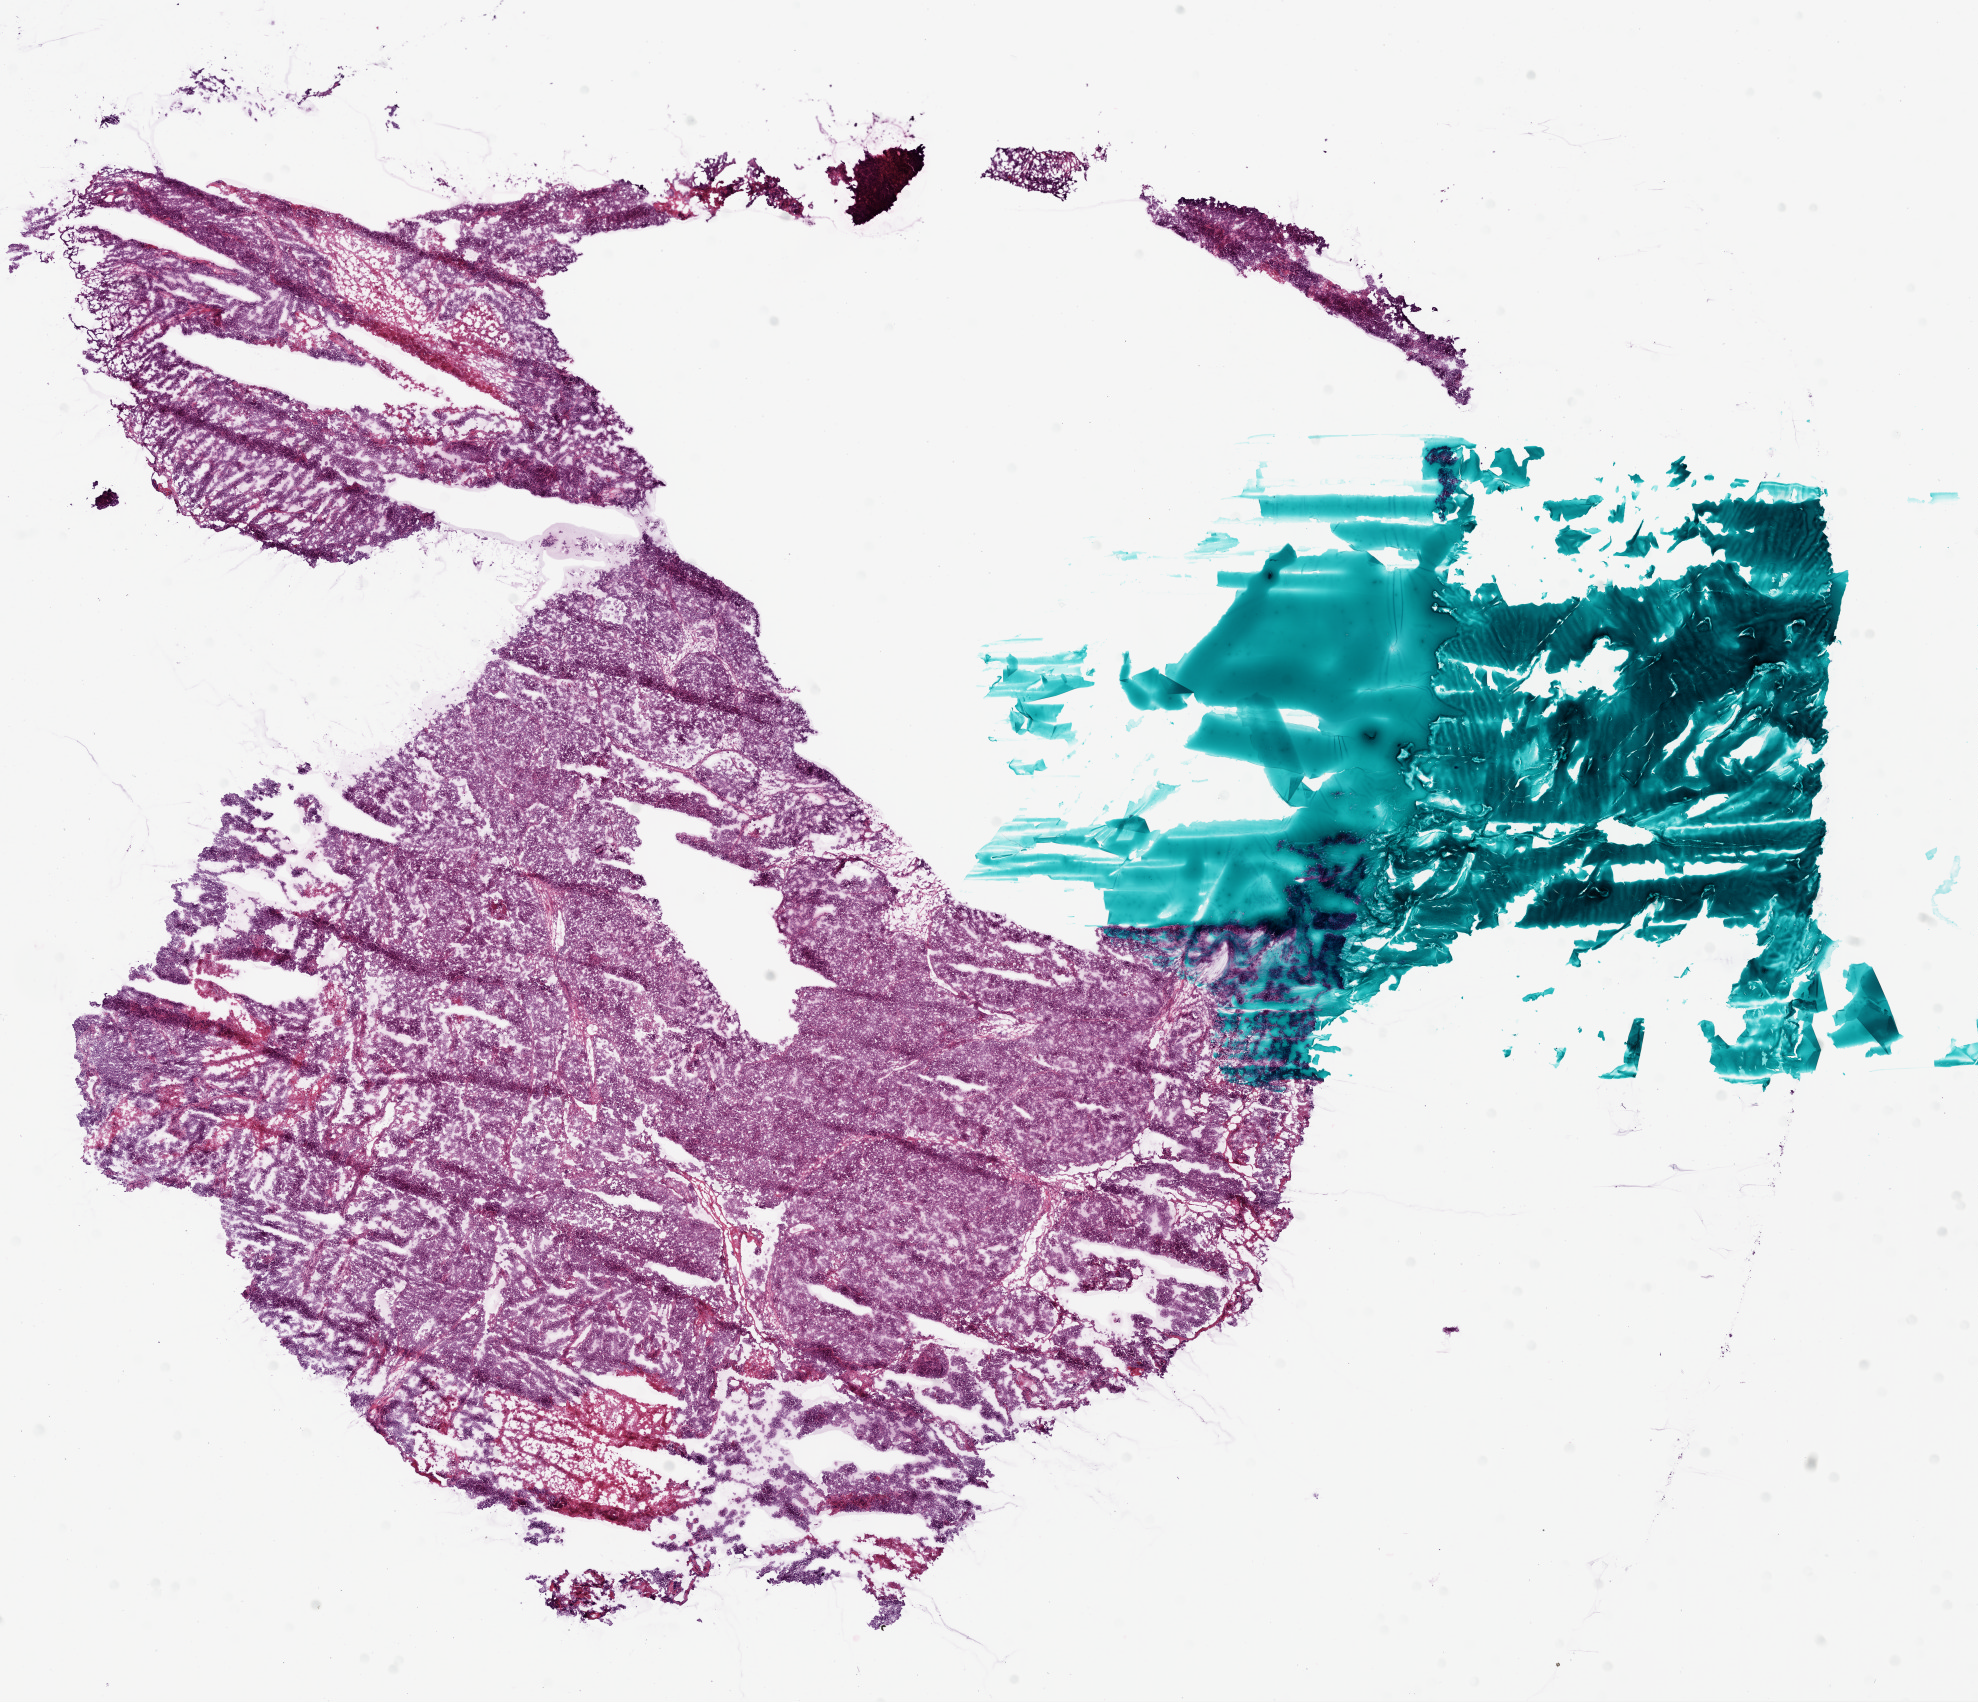
H&E whole-slide image — a low-resolution overview of the entire scanned area, about 16.0 x 13.7 mm, frozen section, sample: primary tumour, ovary. Female, age 44 years at initial diagnosis. Histologic grade: G3 (poorly differentiated). Slide review estimates, as recorded: tumour cells 90%, tumour nuclei 99%, normal cells 0%, stromal cells 2%, necrosis 8%.
- laterality: bilateral
- FIGO stage: IIIB
- diagnosis: Serous cystadenocarcinoma, NOS